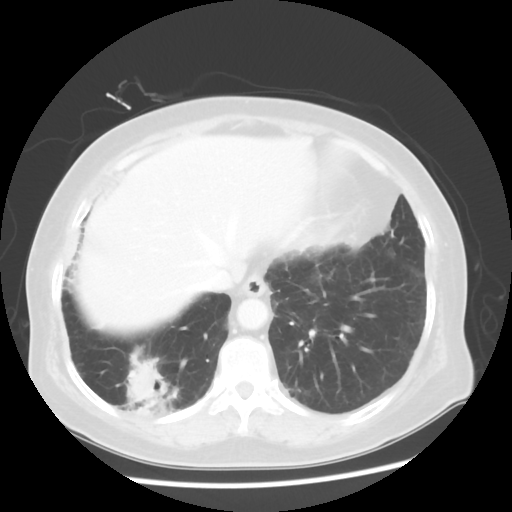
Chest CT, one axial slice. Slice 15 of 56 in the series (ordered by position). Reconstruction kernel STANDARD. 120 kVp. Lung window (W 1500 / L -600 HU). 5 mm slice thickness. 512 × 512 image matrix, field of view 360 × 360 mm. Female patient, age 64 years. From the clinical record (not read from this slice): clinical TNM (as recorded): Tis N0 M0.
Annotated regions visible in this slice (bounding box drawn by a radiologist):
- lung tumour (recorded histology: adenocarcinoma): bounding box (x1, y1, x2, y2) in pixels: (114, 339, 191, 443)